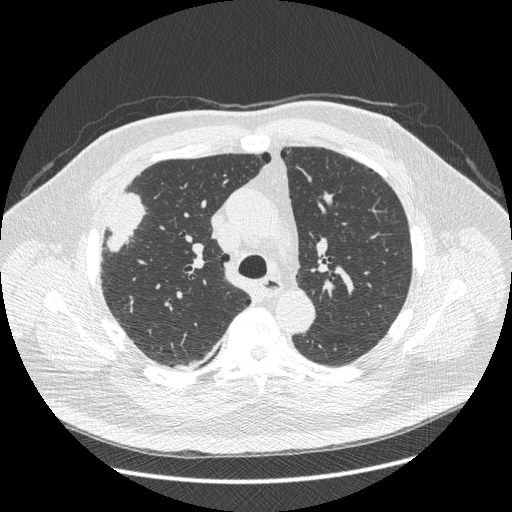
Chest CT (low-dose screening protocol), one axial image, third screening round (two years after baseline), lung window (W 1500 / L -600 HU), standard (soft-tissue) reconstruction kernel (STANDARD), 120 kVp, slice 137 of 426 in the series. Male participant, aged 66 years at enrolment. Current smoker at enrolment.
- Expert reader's lesion annotation, bounding box <87,192,146,267> (left, top, right, bottom; pixels).
- Screening reader's record for this exam (one nodule recorded; not confirmed to be the boxed lesion): non-calcified nodule or mass ≥4 mm, right upper lobe, 48 × 25 mm, spiculated (stellate) margins, soft tissue attenuation, pre-existing on the prior screen: no.
- Later outcome: lung cancer diagnosed 35 days after this screen — non-small cell carcinoma, right upper lobe, stage IV (AJCC 6th edition), 50 mm at pathology.